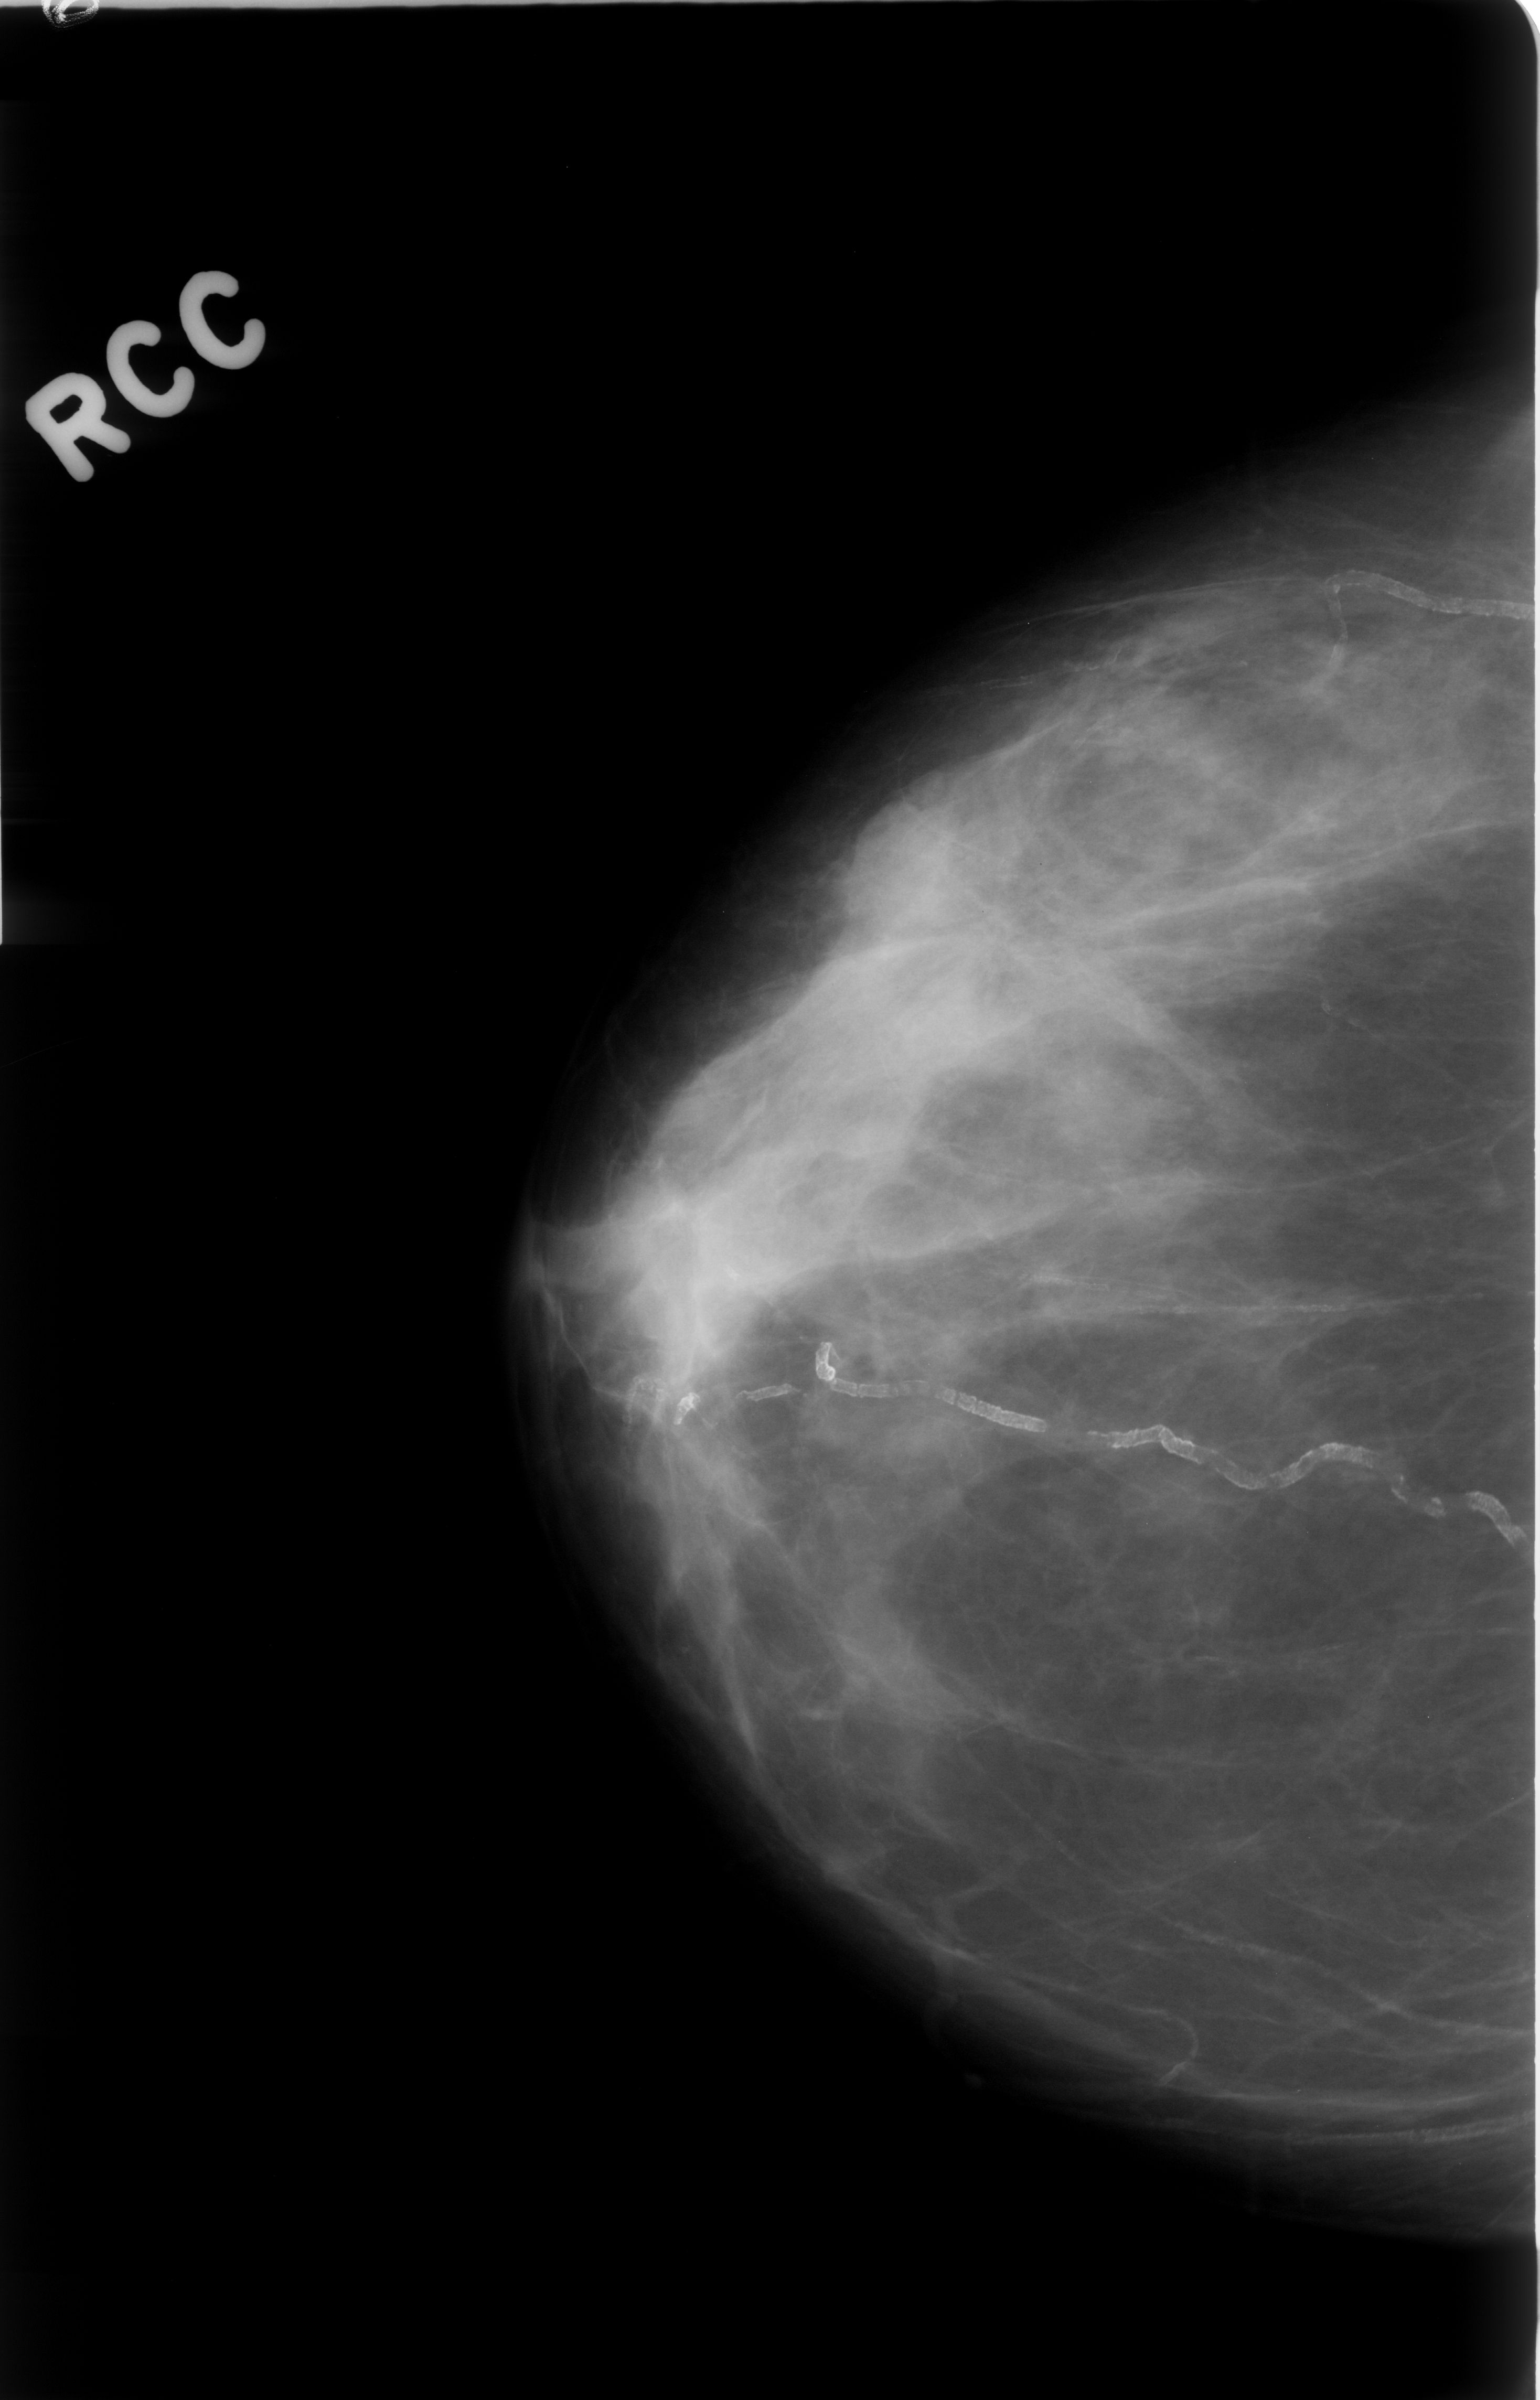
Scanned film-screen mammogram; right breast; CC view; BI-RADS breast density category 2 (scale 1–4); 1540 × 2400 image matrix.
Expert-marked regions of interest on this film, with their recorded descriptors:
- mass, shape architectural distortion; BI-RADS assessment category 4; subtlety rating 4 on a 1 (subtle) to 5 (obvious) scale; benign; no additional work-up was recommended (outcome (as recorded, no biopsy): benign without callback): bounding box (x1, y1, x2, y2) in pixels: (950, 879, 1137, 1058)